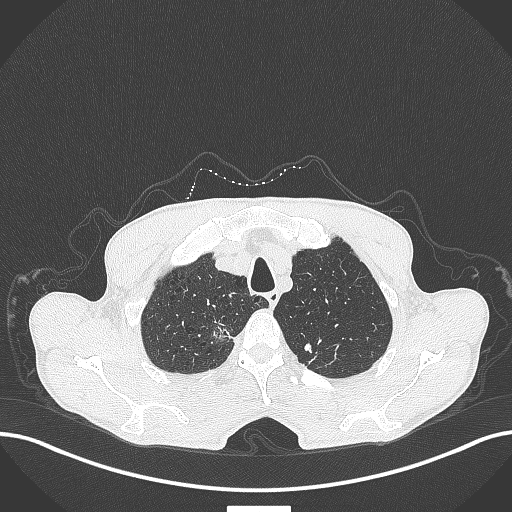
Chest CT, one axial slice; slice 371 of 445 in the series (ordered by position); reconstruction kernel B70f; lung window (W 1500 / L -600 HU); 1 mm slice thickness; 512 × 512 image matrix. Patient: male, 70 years. Case-level facts recorded for this patient, not image findings: clinical TNM (as recorded): T1a N0 M0; histopathological grade: G1-2.
Annotated regions visible in this slice (rectangle marked by the reading radiologist):
- lung tumour (recorded histology: adenocarcinoma): bounding box [x1, y1, x2, y2] px = [208, 318, 244, 345]